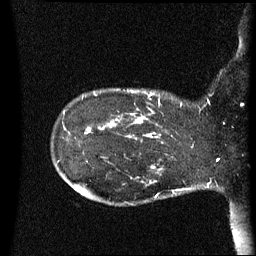
Breast MRI (dynamic contrast-enhanced), one sagittal slice. Position 14 of 60 along the scan axis. Dynamic contrast-enhanced series, image 2 of 3 at this slice position (ordered by acquisition). 1.5 T. TE 4.2 ms, TR 8.4 ms. 2.5 mm slice thickness. 256 × 256 image matrix, field of view 220 × 220 mm. Female patient, age 41 years. From the clinical record (not read from this slice): setting: breast cancer imaged before/during neoadjuvant chemotherapy; receptor status: HER2-positive.
Annotated regions visible in this slice (semi-automatically segmented with operator editing):
- analysis volume of interest (the breast-tissue region the enhancement analysis was run in; not a lesion): bounding box <122,90,195,137> (left, top, right, bottom; pixels)
- tumour enhancement mask (voxels above the 70 % enhancement threshold inside the analysis volume of interest): <131,92,182,137>